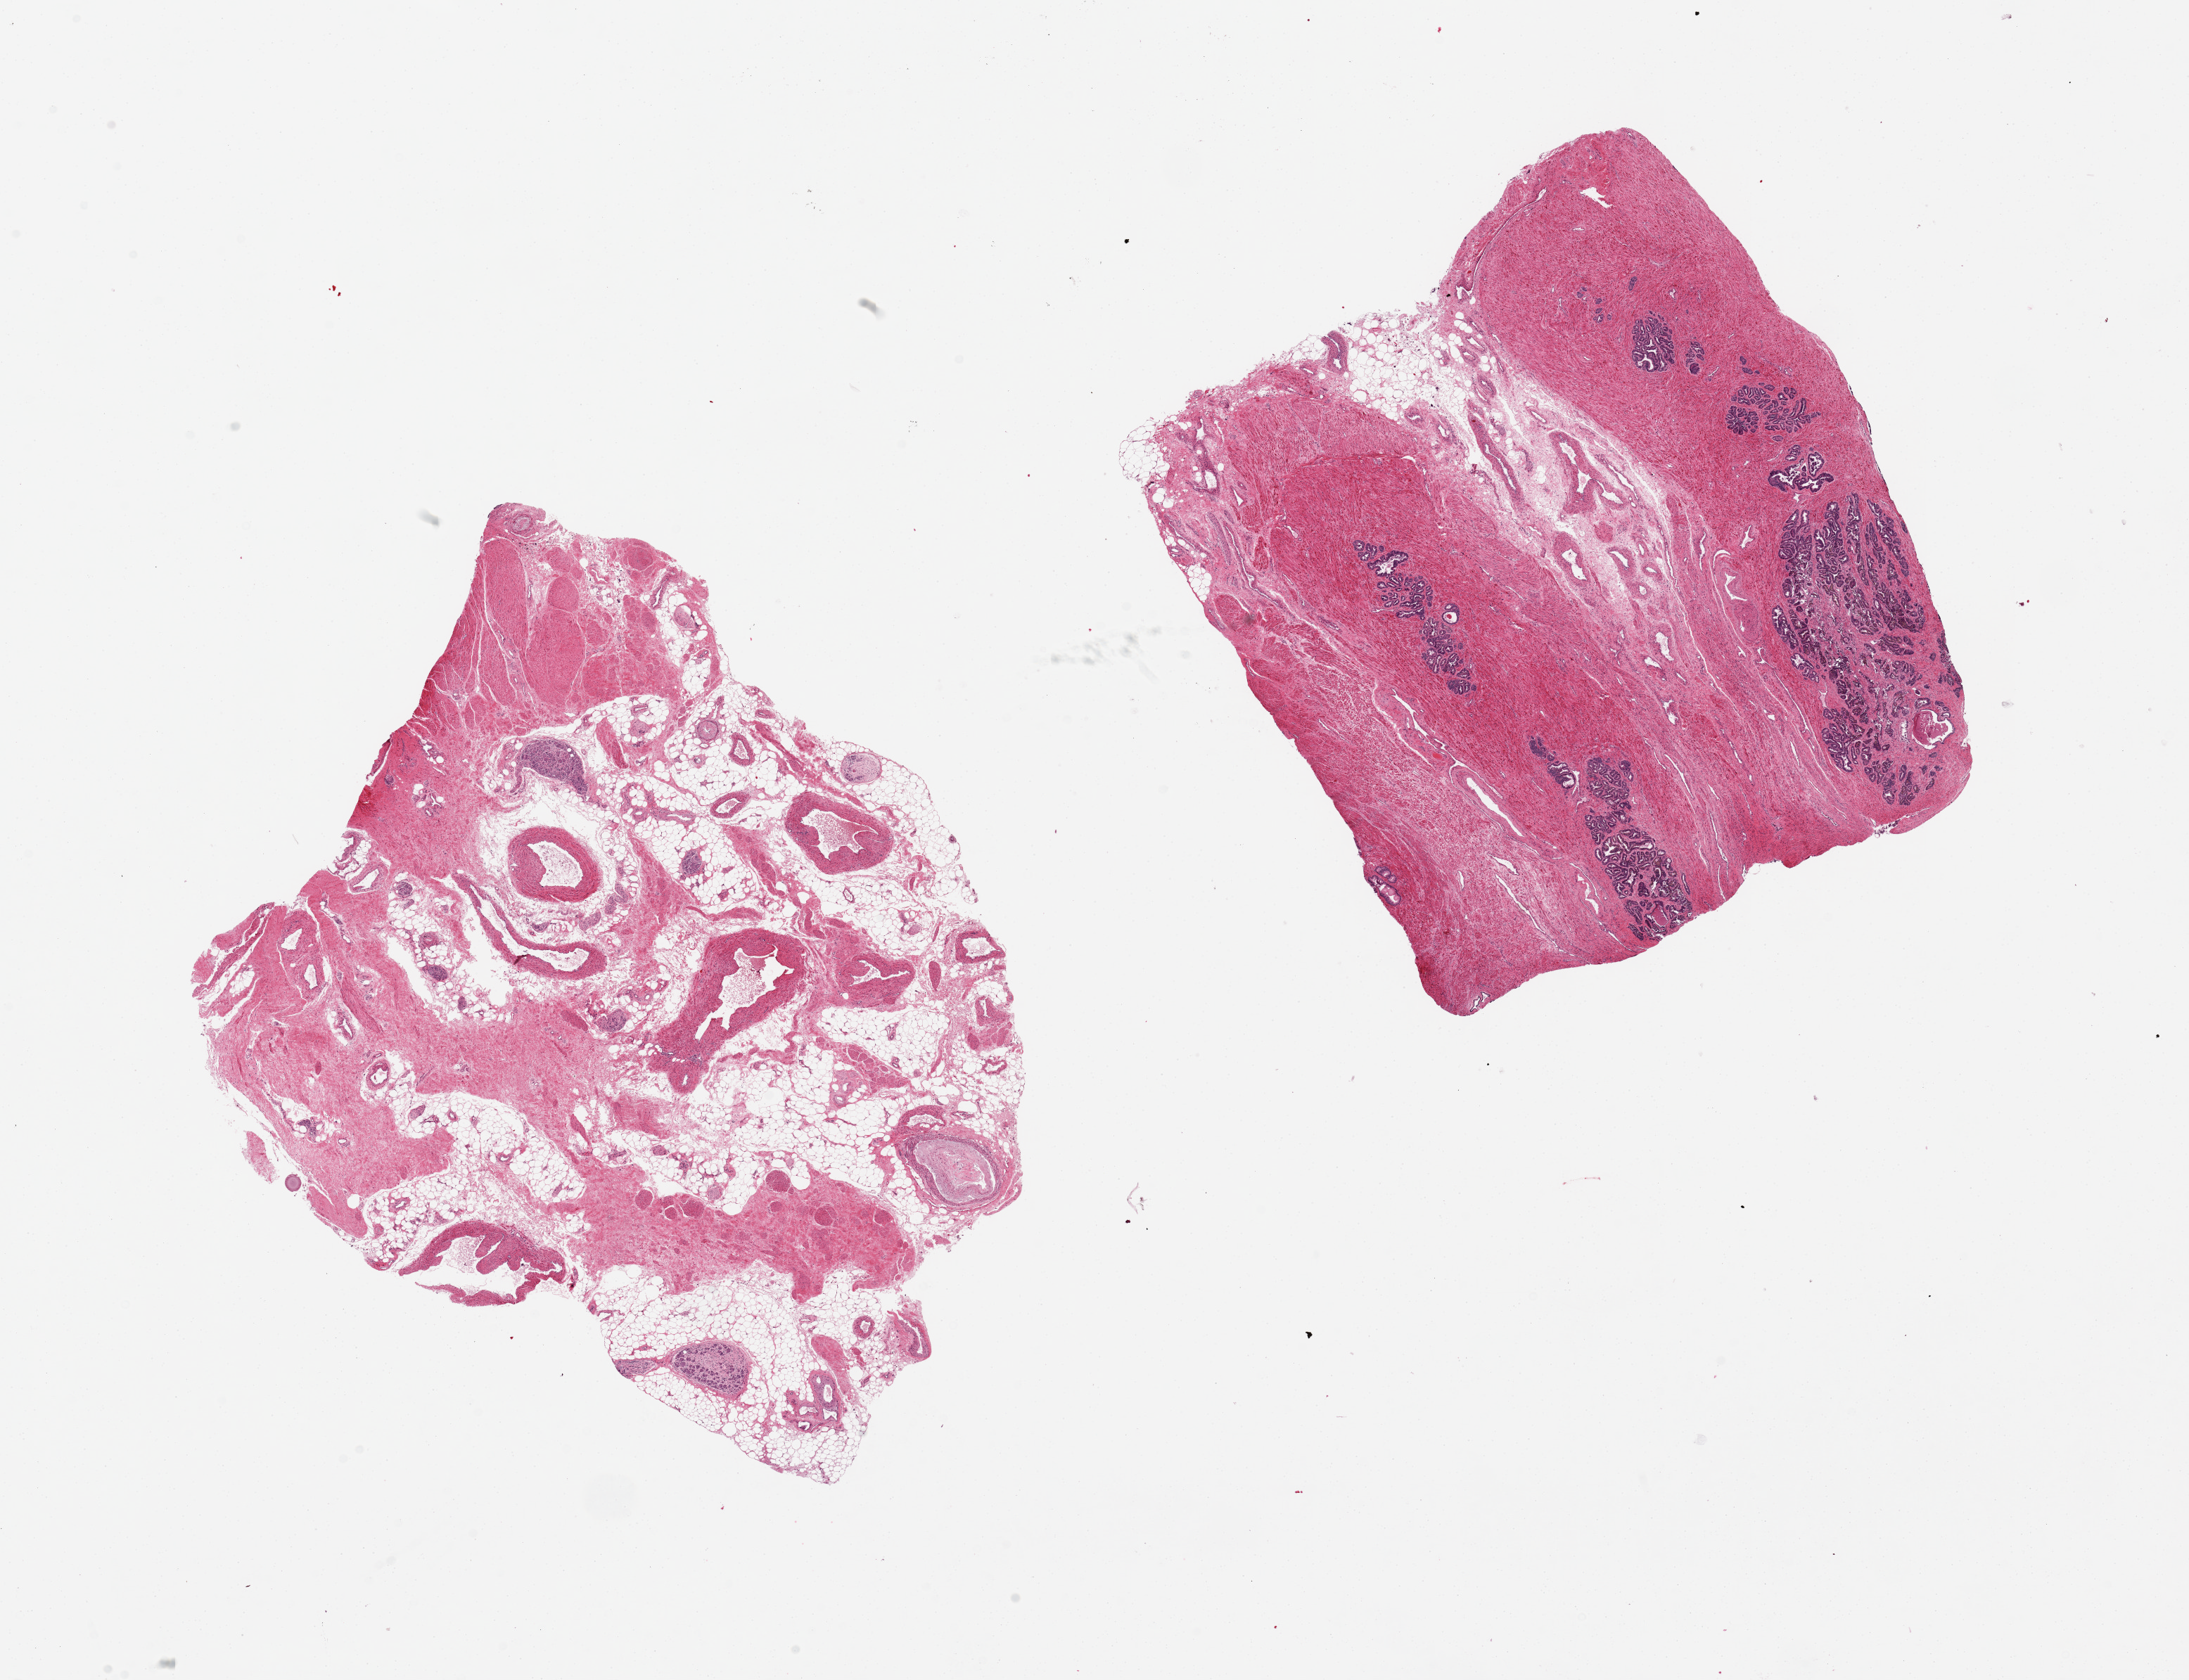
Haematoxylin and eosin whole-slide image, a low-resolution overview of the entire scanned area, about 24.6 x 18.9 mm; PAXgene-fixed, paraffin-embedded tissue; section of prostate (target tissue); tissue donor sample. Donor: male.
Pathologist's review note for this sample: 2 pieces, 10x8.5 & 9x8mm; 1 is seminal vesicle; other is fibroadipose, muscle and ganglia; no prostate tissue.